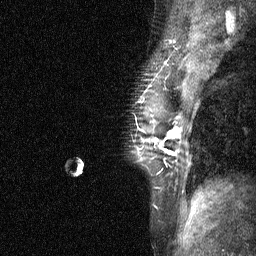
Breast MRI (dynamic contrast-enhanced), one sagittal slice; slice 45 of 64 in the series (ordered by position); dynamic contrast-enhanced study with each time point stored as its own series, time point 3 of 4 at this slice position (ordered by acquisition time); 1.5 T; TE 4.8 ms, TR 27 ms; 2 mm slice thickness; 256 × 256 image matrix, field of view 180 × 180 mm. Patient: female, 44 years. Case-level facts recorded for this patient, not image findings: setting: breast cancer imaged before/during neoadjuvant chemotherapy; receptor status: HR-positive, HER2-negative.
Structures marked on this image (semi-automatic segmentation, software-assisted and operator-edited):
- analysis volume of interest (the breast-tissue region the enhancement analysis was run in; not a lesion): bounding box [x1, y1, x2, y2] px = [127, 117, 185, 188]
- tumour enhancement mask (voxels above the 90 % enhancement threshold inside the analysis volume of interest): [154, 129, 181, 155]